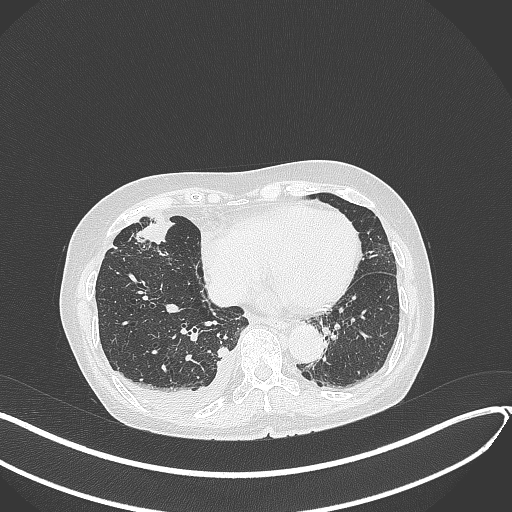
Chest CT, one axial slice; slice 124 of 418 in the series (ordered by position); reconstruction kernel B70f; lung window (W 1500 / L -600 HU); 1 mm slice thickness; 512 × 512 image matrix, field of view 400 × 400 mm. Patient: female, 75 years. From the clinical record (not read from this slice): clinical TNM (as recorded): T2a N3 M0.
Structures marked on this image (bounding box drawn by a radiologist):
- lung tumour (recorded histology: adenocarcinoma): bounding box (x1, y1, x2, y2) in pixels: (137, 215, 179, 249)